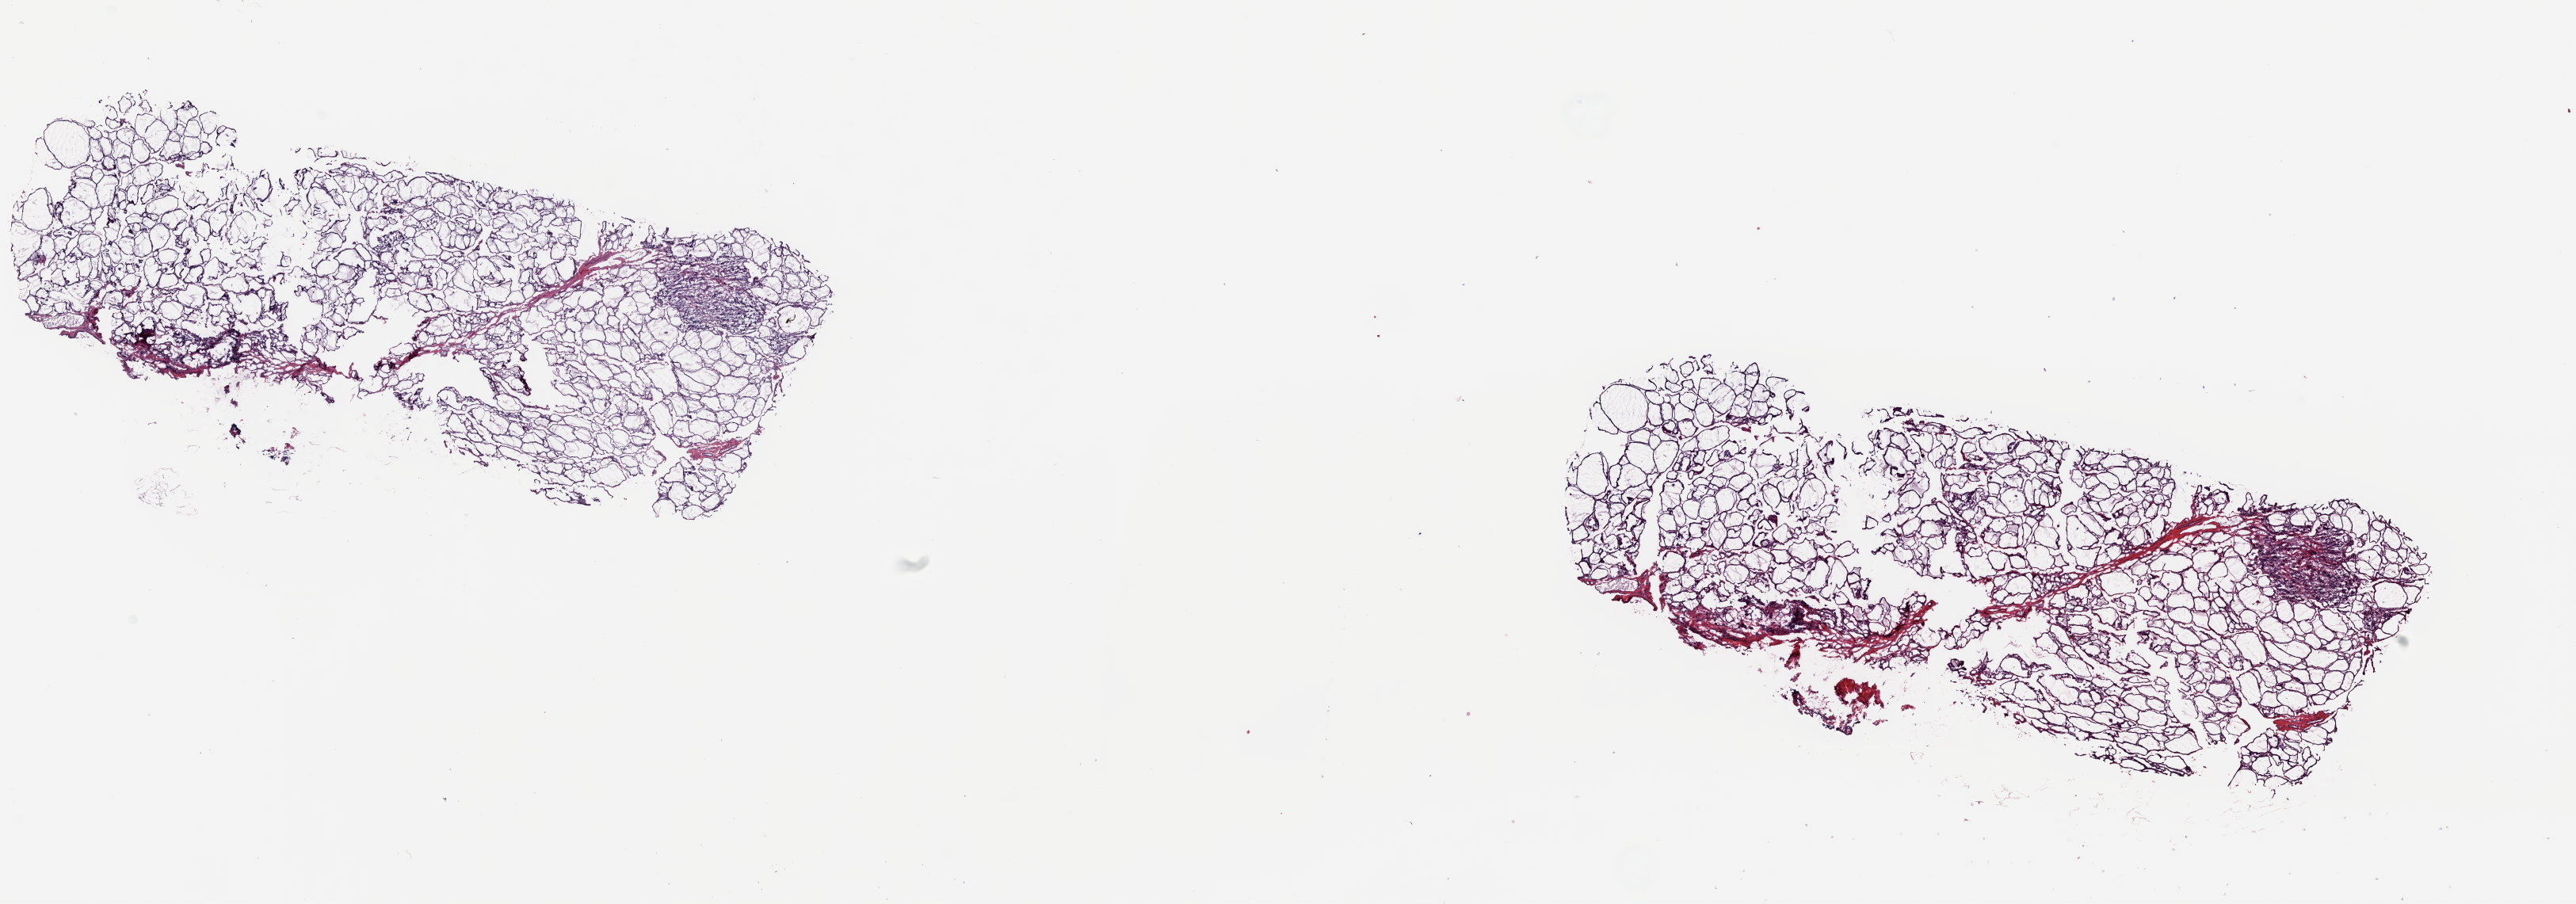
Digitized H&E tissue section (whole slide), a low-resolution overview of the entire scanned area, about 25.8 x 9.1 mm, frozen section from the top of the tissue portion, thyroid, solid tissue normal (non-tumour tissue) sample. Female patient; age at initial diagnosis 28 years. Composition of this section per pathologist review: tumour cells 0%, tumour nuclei 0%, normal cells 100%, stromal cells 0%, necrosis 0%. Inflammatory infiltration, as recorded: lymphocyte infiltration 0%, monocyte infiltration 0%, neutrophil infiltration 0%.
• this section: solid tissue normal sample (biorepository sample class)
• patient diagnosis: Papillary adenocarcinoma, NOS